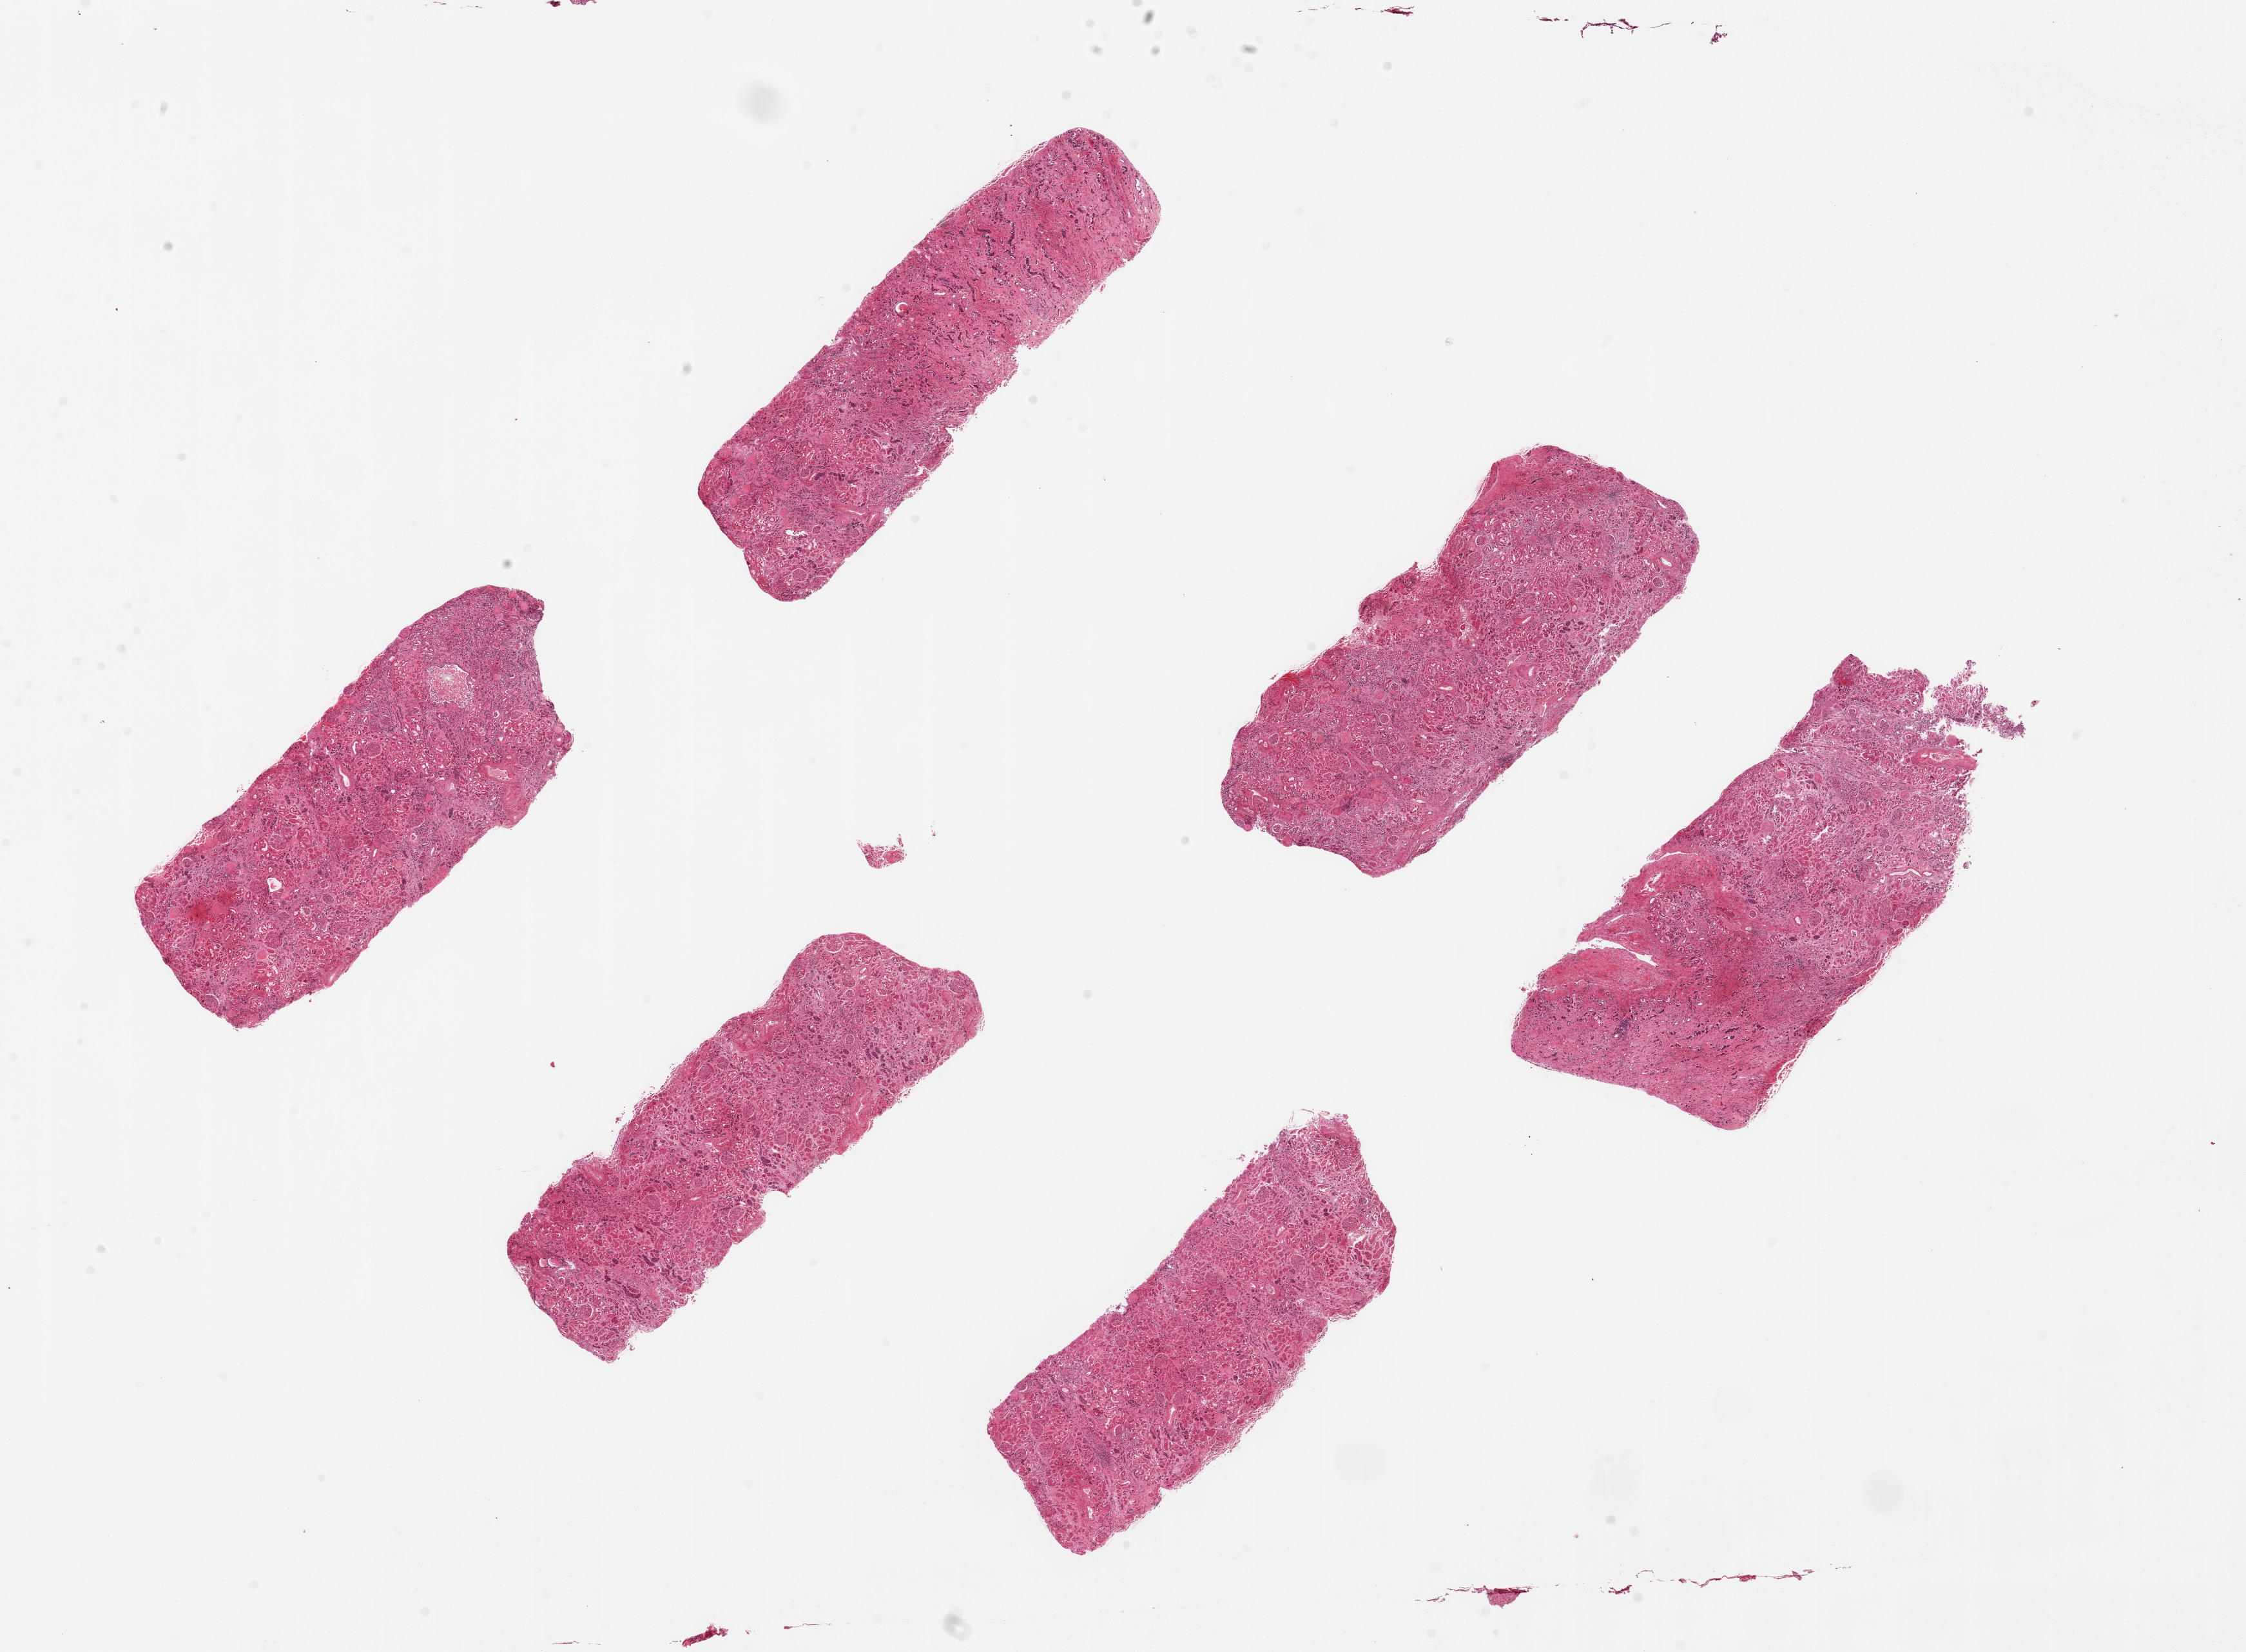
Digitized haematoxylin and eosin-stained section, whole scanned area (about 27.6 x 20.3 mm, slide scanned at 20x) shown as a low-resolution overview; PAXgene-fixed, paraffin-embedded tissue; target tissue: renal cortex; tissue donor sample. Donor: female.
• pathologist's review note for this sample: 6 pieces; up to 7x3.5mm; moderate mixture with medulla in 2/6; moderate glomerulosclerosis